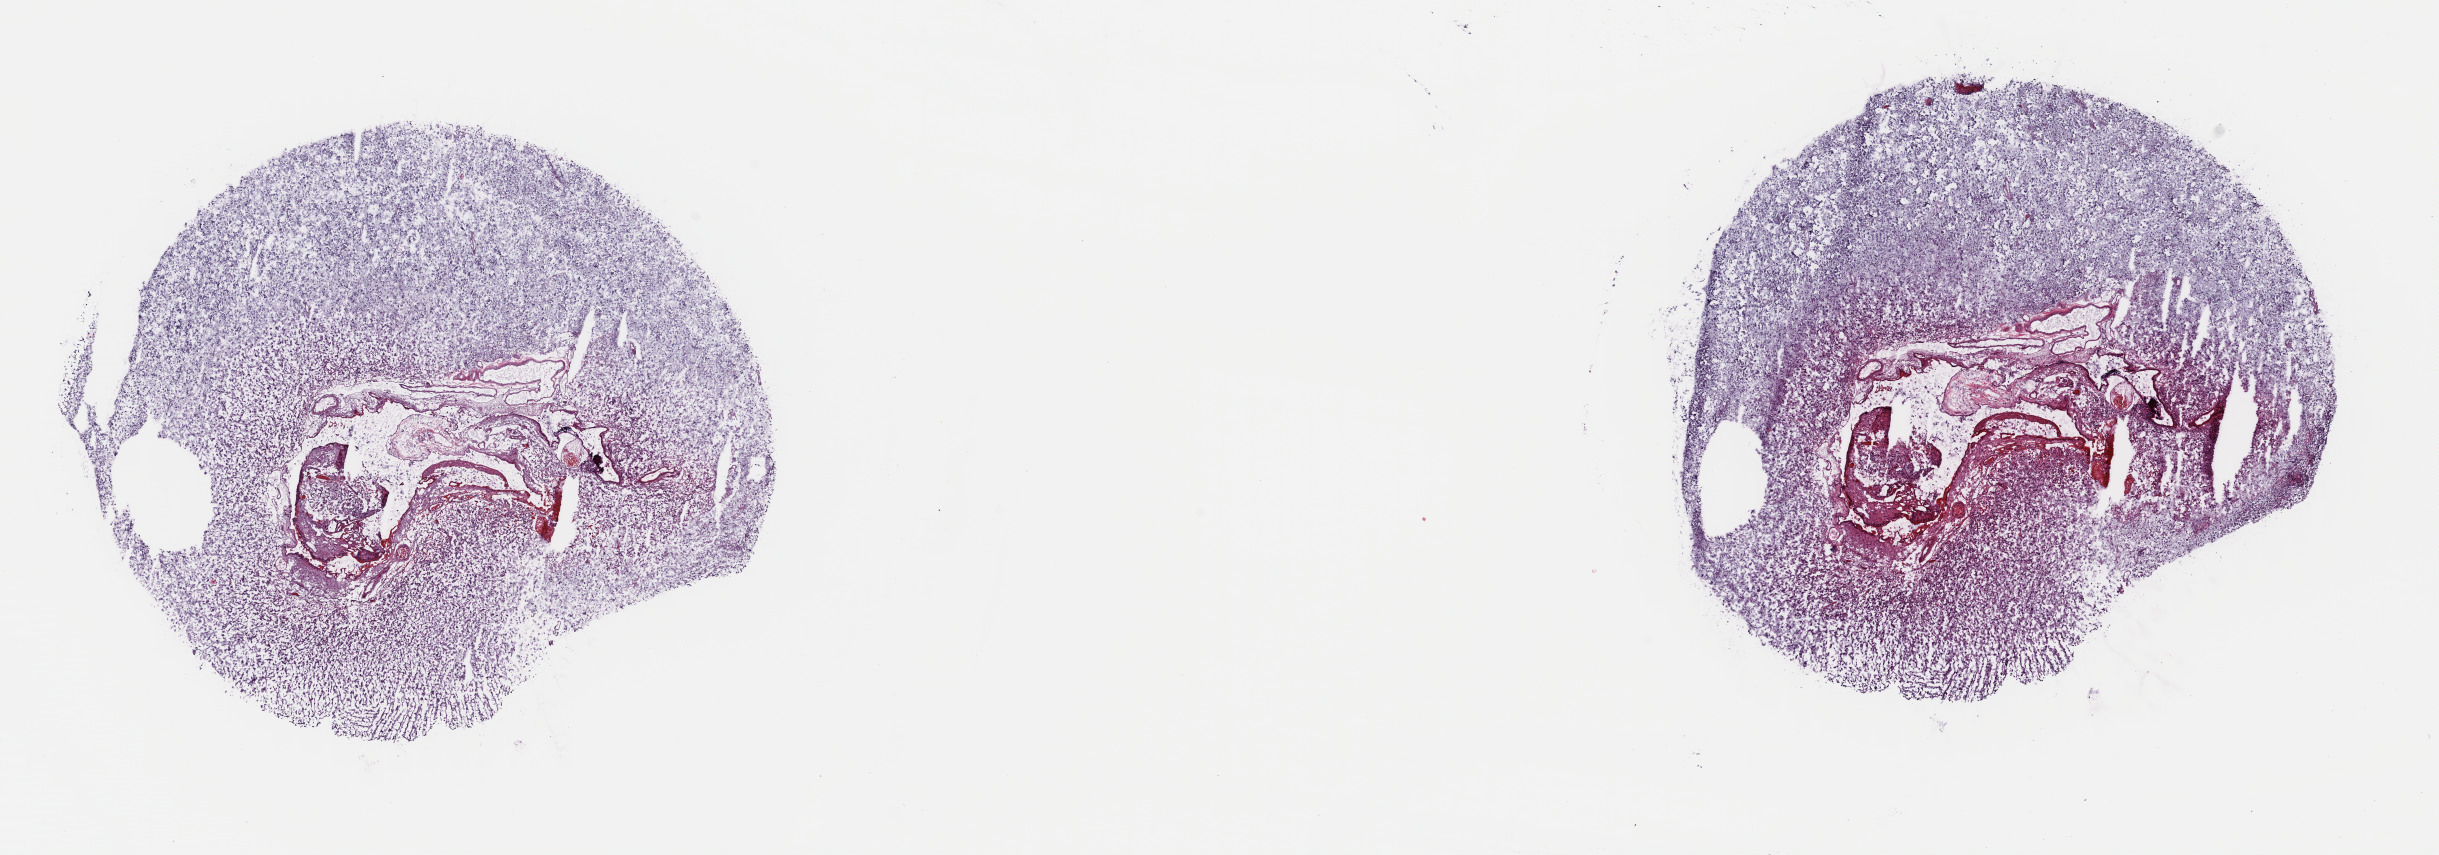
Whole-slide histology image, Hematoxylin and eosin (H&E) stained — low-resolution overview of the scanned area, about 19.2 x 6.7 mm (slide scanned at 40x). Frozen section from the top of the tissue portion. Primary tumour sample from the brain. Female, age 48 years at initial diagnosis. Histologic grade: G3 (poorly differentiated). Composition of this section per pathologist review: tumour cells 80%, tumour nuclei 80%, normal cells 5%, stromal cells 15%, necrosis 0%. Infiltration values recorded for this section: lymphocyte infiltration 0%, monocyte infiltration 0%, neutrophil infiltration 0%.
Diagnosis: Oligodendroglioma, anaplastic (cerebrum).